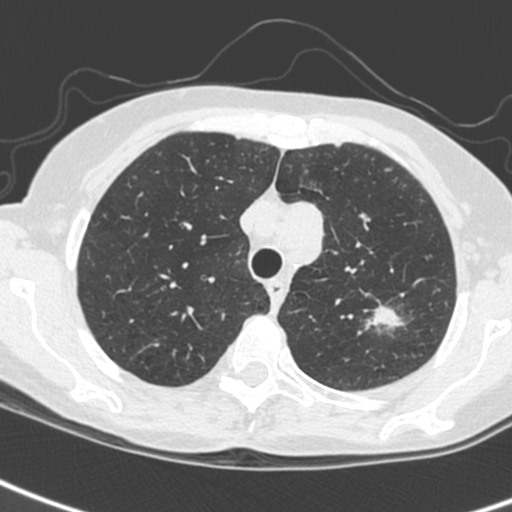
Axial slice from a low-dose chest CT screening exam, baseline screening round, lung window (W 1500 / L -600 HU), 1.3 mm slice thickness, 120 kVp, slice 45 of 242 in the series. Female participant, aged 61 years at enrolment. Current smoker at enrolment.
Expert reader's lesion annotation, bounding box <348,297,412,349> (left, top, right, bottom; pixels). The screening reader recorded 2 non-calcified nodules or masses ≥4 mm on this exam (left upper lobe, left upper lobe); which of them this box marks is not recorded. Official screen result: positive, change unspecified: nodule(s) >= 4 mm or enlarging nodule(s), mass(es), or other non-specific abnormalities suspicious for lung cancer. Lung cancer was diagnosed 29 days after this screen: small cell carcinoma, NOS, left upper lobe, stage IV (AJCC 6th edition).